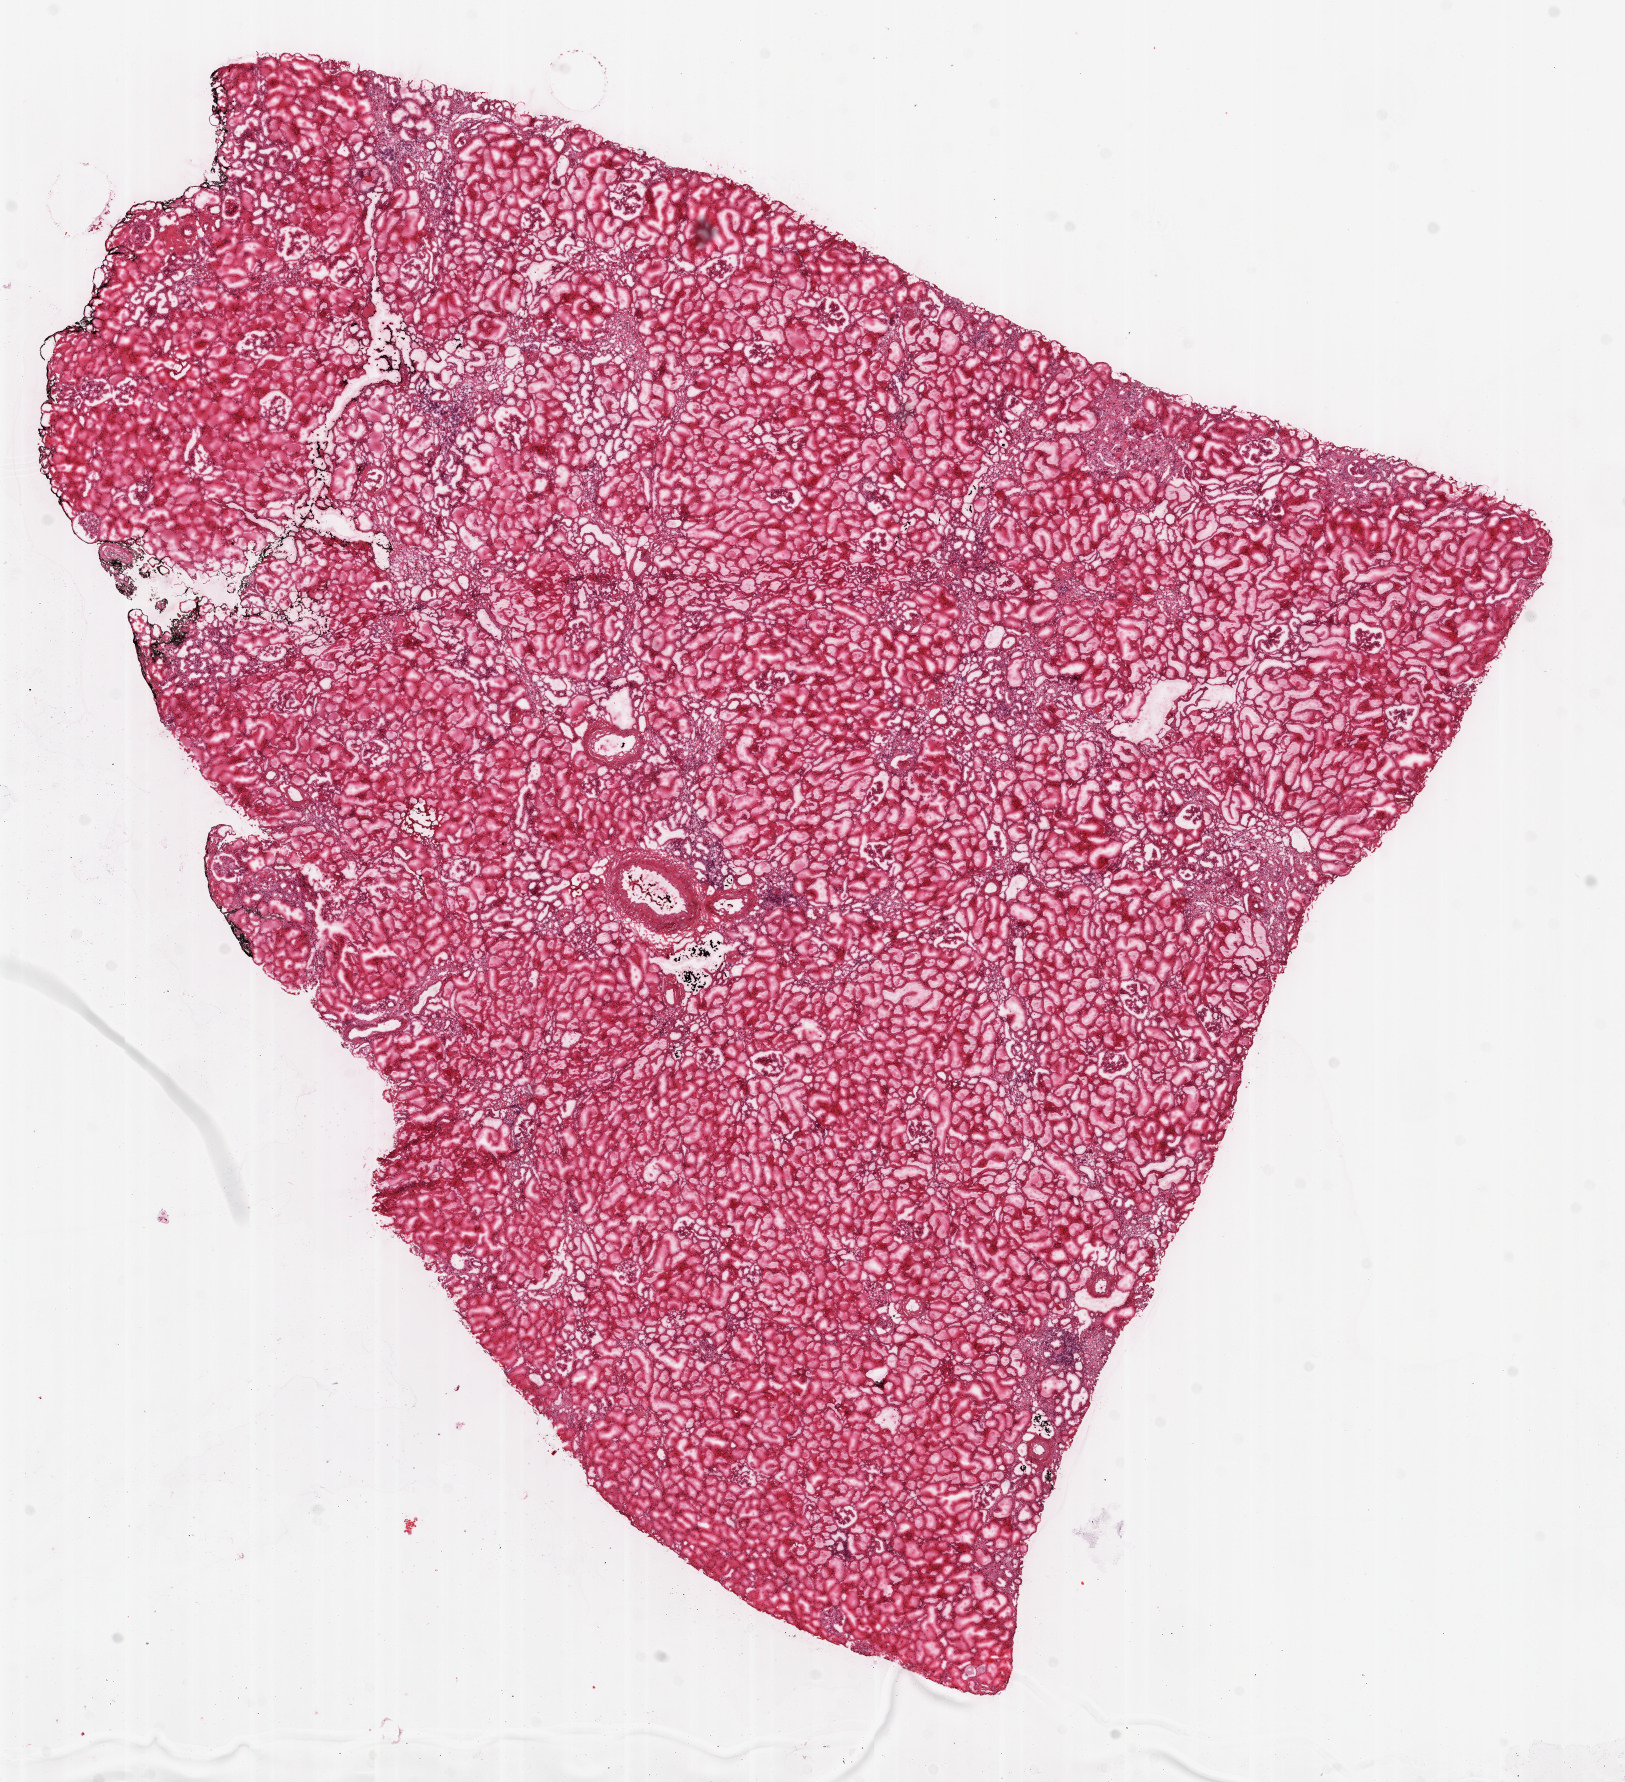
H&E-stained whole-slide image, shown as a low-resolution overview of the whole scanned area (about 13.0 x 14.3 mm, slide scanned at 20x), frozen section from the top of the tissue portion, kidney, solid tissue normal (non-tumour tissue) sample. Male, age 56 years at initial diagnosis.
This section: solid tissue normal sample (biorepository sample class). Patient diagnosis: Clear cell adenocarcinoma, NOS.